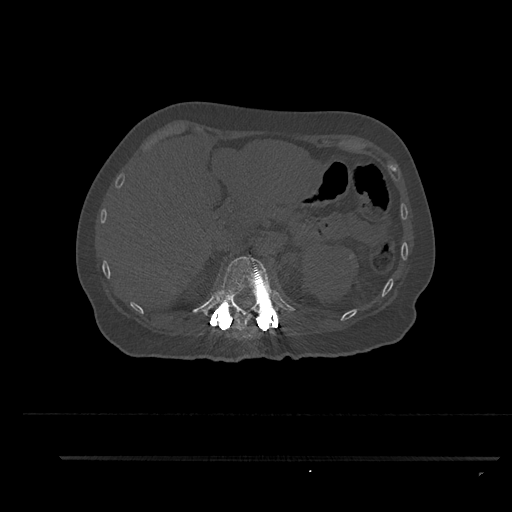
CT including the spine, one axial slice; position 267 of 797 along the scan axis; reconstruction kernel Br40s/3; 120 kVp; bone window (W 1800 / L 400 HU); 0.5 mm slice thickness; 512 × 512 image matrix, field of view 408 × 408 mm. Patient: female, 44 years. From the clinical record (not read from this slice): primary cancer: renal.
Annotated regions visible in this slice (semi-automatic segmentation, software-assisted and operator-edited):
- T12 vertebra: bounding box <217,255,281,328> (left, top, right, bottom; pixels)